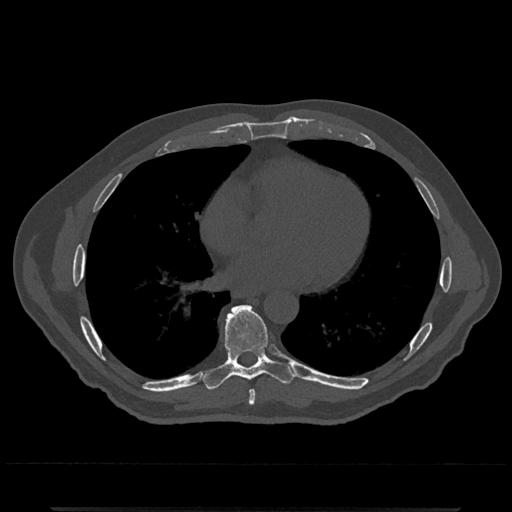
CT including the spine, one axial slice. Slice 675 of 797 in the series (ordered by position). Bone window (W 1800 / L 400 HU). 512 × 512 image matrix, field of view 393 × 393 mm. Patient: male, 67 years. From the clinical record (not read from this slice): primary cancer: prostate.
Outlined on this slice (semi-automatic segmentation, software-assisted and operator-edited):
- T7 vertebra: bounding box (x1, y1, x2, y2) in pixels: (248, 390, 256, 406)
- T8 vertebra: (203, 305, 296, 390)